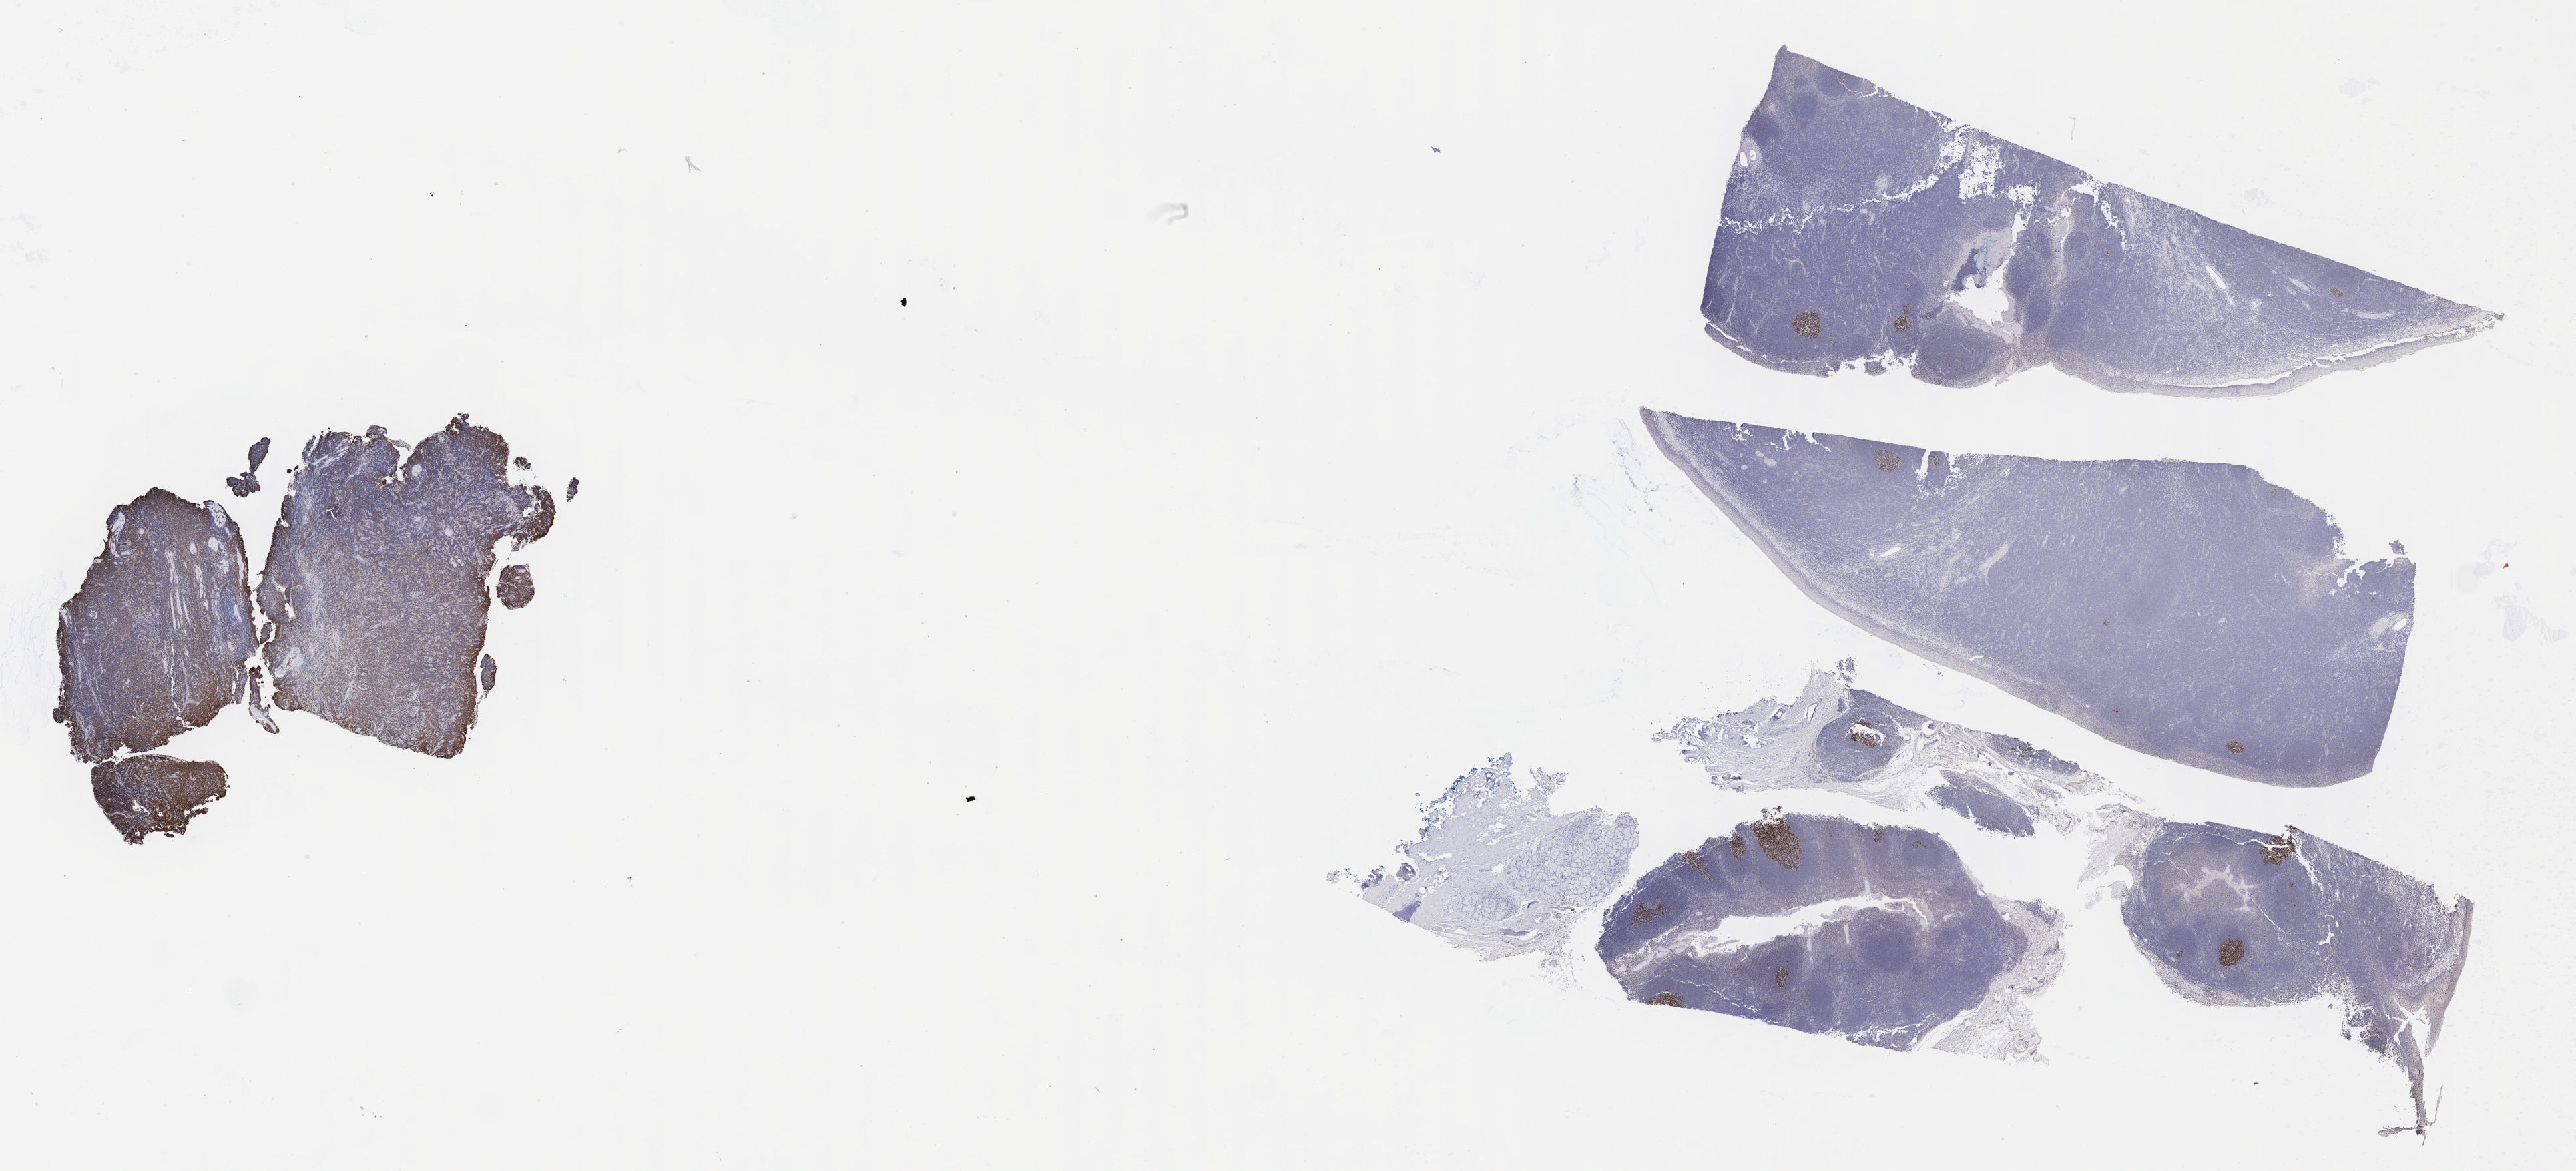
Immunohistochemistry (IHC) whole-slide image stained for BCL6, shown as a low-resolution overview of the whole scanned area (about 31.2 x 14.2 mm). Specimen: tumor tissue. Site: cranium. Male patient; age at initial diagnosis 8 years.
Diagnosis: Burkitt lymphoma, NOS.